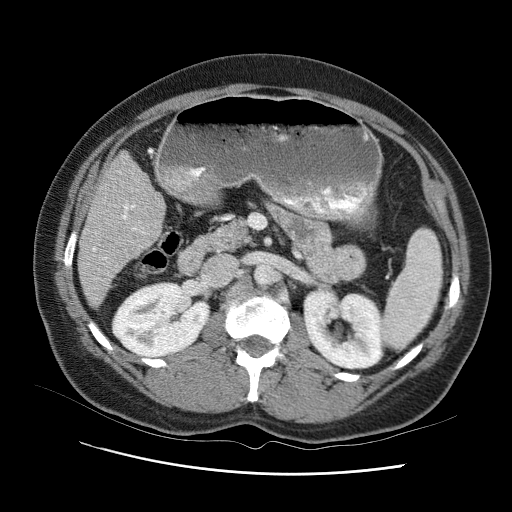
Contrast-enhanced abdominal CT (liver protocol), one axial slice. Position 37 of 95 along the scan axis. 120 kVp. One of 2 acquisitions stored at this slice position. Soft-tissue window (W 400 / L 40 HU). 512 × 512 image matrix, field of view 360 × 360 mm. Case-level facts recorded for this patient, not image findings: diagnosis: hepatocellular carcinoma (patient treated with transarterial chemoembolisation; whether this scan precedes or follows treatment is not stated here); TNM stage (as recorded): Stage-I; Child-Pugh class: B; tumour differentiation: moderately differentiated; tumour nodularity: uninodular.
Outlined on this slice (semi-automatically segmented with operator editing):
- liver parenchyma outside the tumour (the mass and vessels are separate outlines, so this box may not span the whole liver): bounding box (x1, y1, x2, y2) in pixels: (76, 142, 168, 318)
- mass: (126, 265, 165, 293)
- liver vessels: (104, 196, 153, 284)